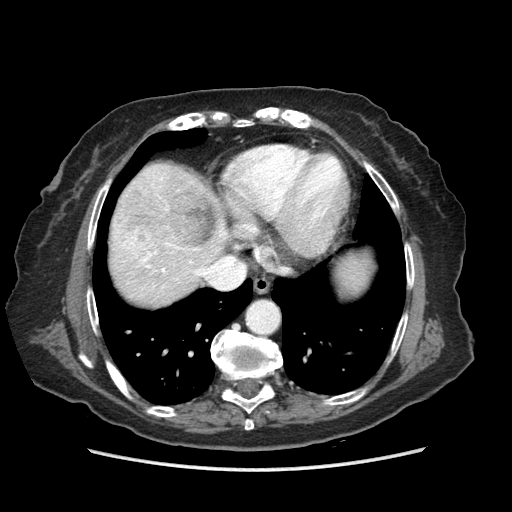
Contrast-enhanced abdominal CT (liver protocol), one axial slice; position 75 of 89 along the scan axis; reconstruction kernel STANDARD; soft-tissue window (W 400 / L 40 HU); 2.5 mm slice thickness; 512 × 512 image matrix, field of view 360 × 360 mm. From the clinical record (not read from this slice): diagnosis: hepatocellular carcinoma (patient treated with transarterial chemoembolisation; whether this scan precedes or follows treatment is not stated here); TNM stage (as recorded): Stage-IIIA; Child-Pugh class: A; tumour size: 11 cm.
Structures marked on this image (semi-automatically segmented with operator editing):
- liver parenchyma outside the tumour (the mass and vessels are separate outlines, so this box may not span the whole liver): bounding box [x1, y1, x2, y2] px = [110, 162, 370, 306]
- mass: [137, 188, 215, 247]
- liver vessels: [123, 178, 225, 276]